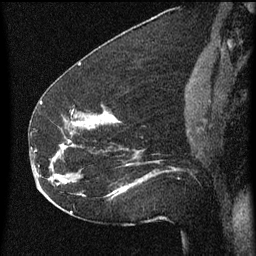
Breast MRI (dynamic contrast-enhanced), one sagittal slice; dynamic contrast-enhanced series, image 2 of 3 at this slice position (ordered by acquisition); 1.5 T; TE 4.2 ms, TR 8 ms; 256 × 256 image matrix, field of view 180 × 180 mm. Female patient, age 52 years.
Annotated regions visible in this slice (semi-automatic segmentation, software-assisted and operator-edited):
- analysis volume of interest (the breast-tissue region the enhancement analysis was run in; not a lesion): bounding box <54,110,178,207> (left, top, right, bottom; pixels)
- tumour enhancement mask (voxels above the 70 % enhancement threshold inside the analysis volume of interest): <61,112,128,191>